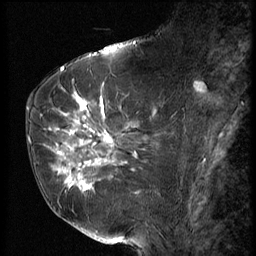
Breast MRI (dynamic contrast-enhanced), one sagittal slice; slice 29 of 56 in the series (ordered by position); 3 images stored at this slice position (order not interpretable as contrast timing); 1.5 T; TE 4.2 ms, TR 9 ms; 2.5 mm slice thickness; 256 × 256 image matrix, field of view 180 × 180 mm. Patient: female, 61 years. From the clinical record (not read from this slice): setting: breast cancer imaged before/during neoadjuvant chemotherapy; receptor status: HR-positive, HER2-negative.
Annotated regions visible in this slice (semi-automatically segmented with operator editing):
- analysis volume of interest (the breast-tissue region the enhancement analysis was run in; not a lesion): bounding box [x1, y1, x2, y2] px = [47, 89, 153, 191]
- tumour enhancement mask (voxels above the 140 % enhancement threshold inside the analysis volume of interest): [49, 97, 134, 189]